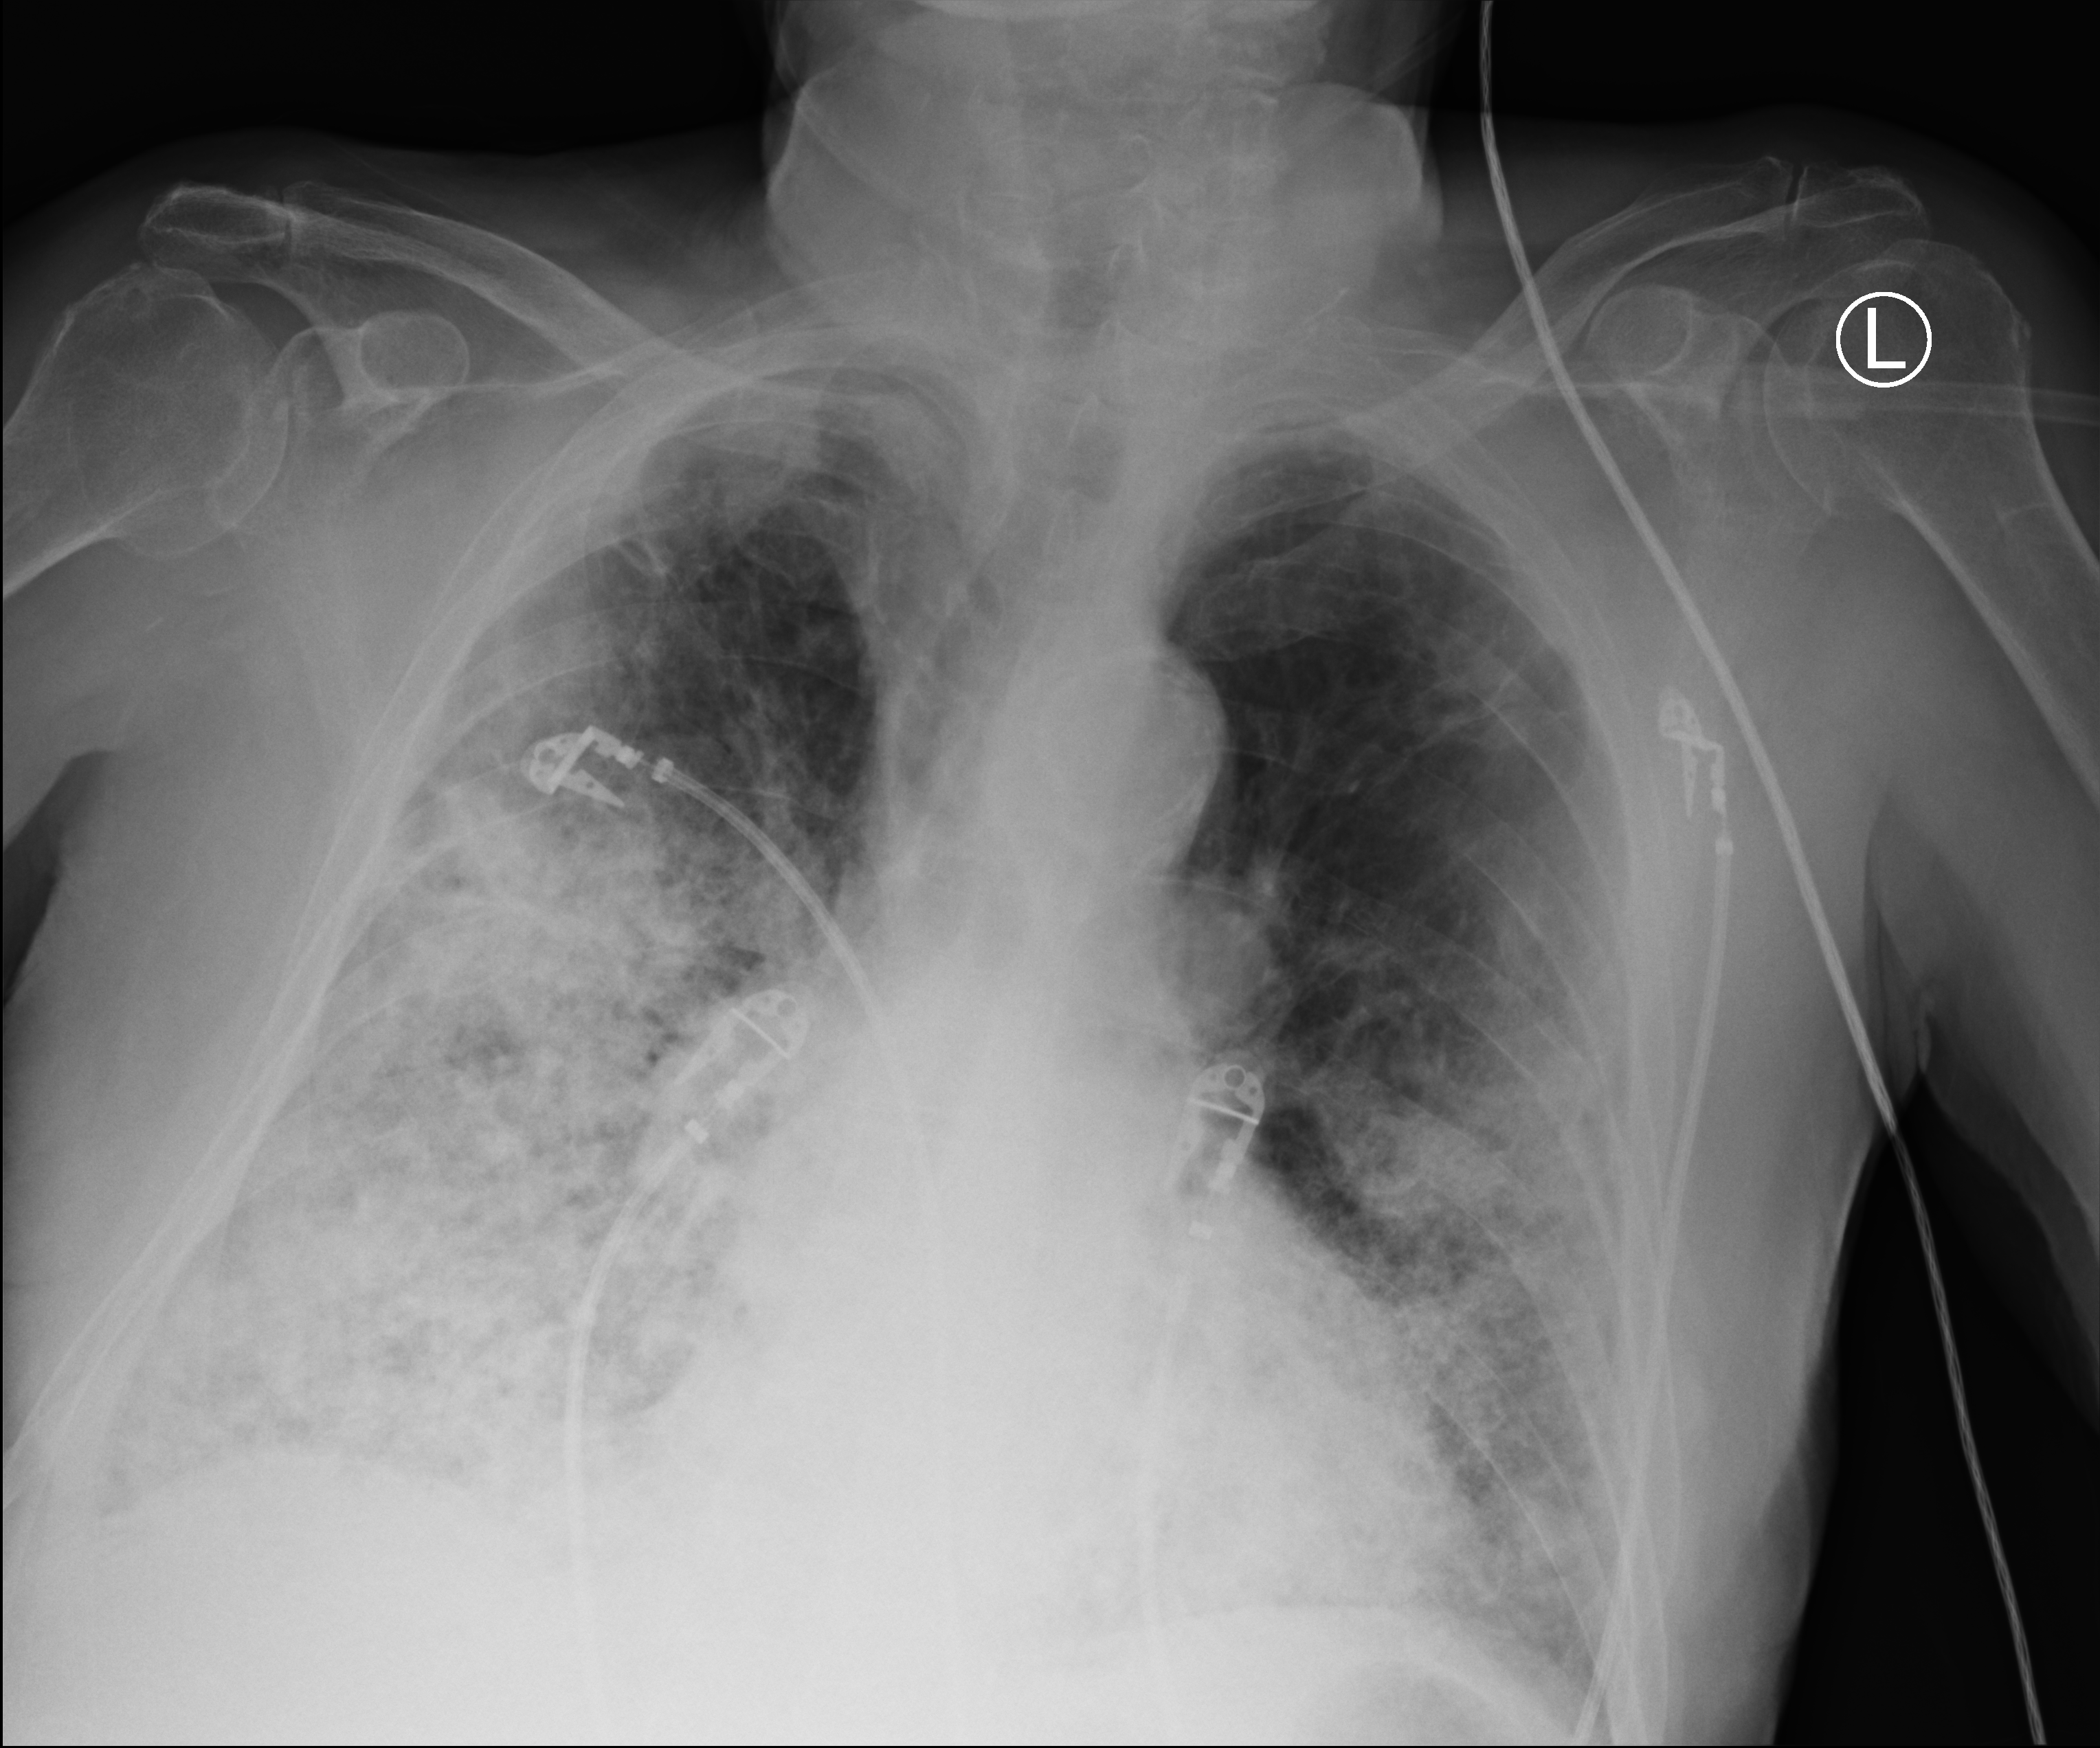
Chest X-ray (portable); anteroposterior (AP) projection. Male patient hospitalised with COVID-19, age 75–90 years.
From the hospital-stay record, not from the radiograph (when in the stay this image was taken is not recorded): chronic kidney disease (admission record): yes.